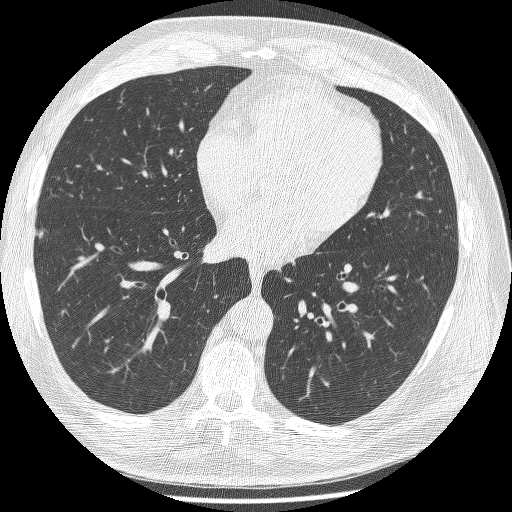
Low-dose screening chest CT, one axial slice; reconstruction kernel BONE; 120 kVp; lung window (W 1500 / L -600 HU); 512 × 512 image matrix, field of view 346 × 346 mm.
Structures marked on this image (outlined manually by an expert reader):
- lesion 1 (tumor, lower lobe of right lung): box from (x=35, y=230) to (x=43, y=239) px